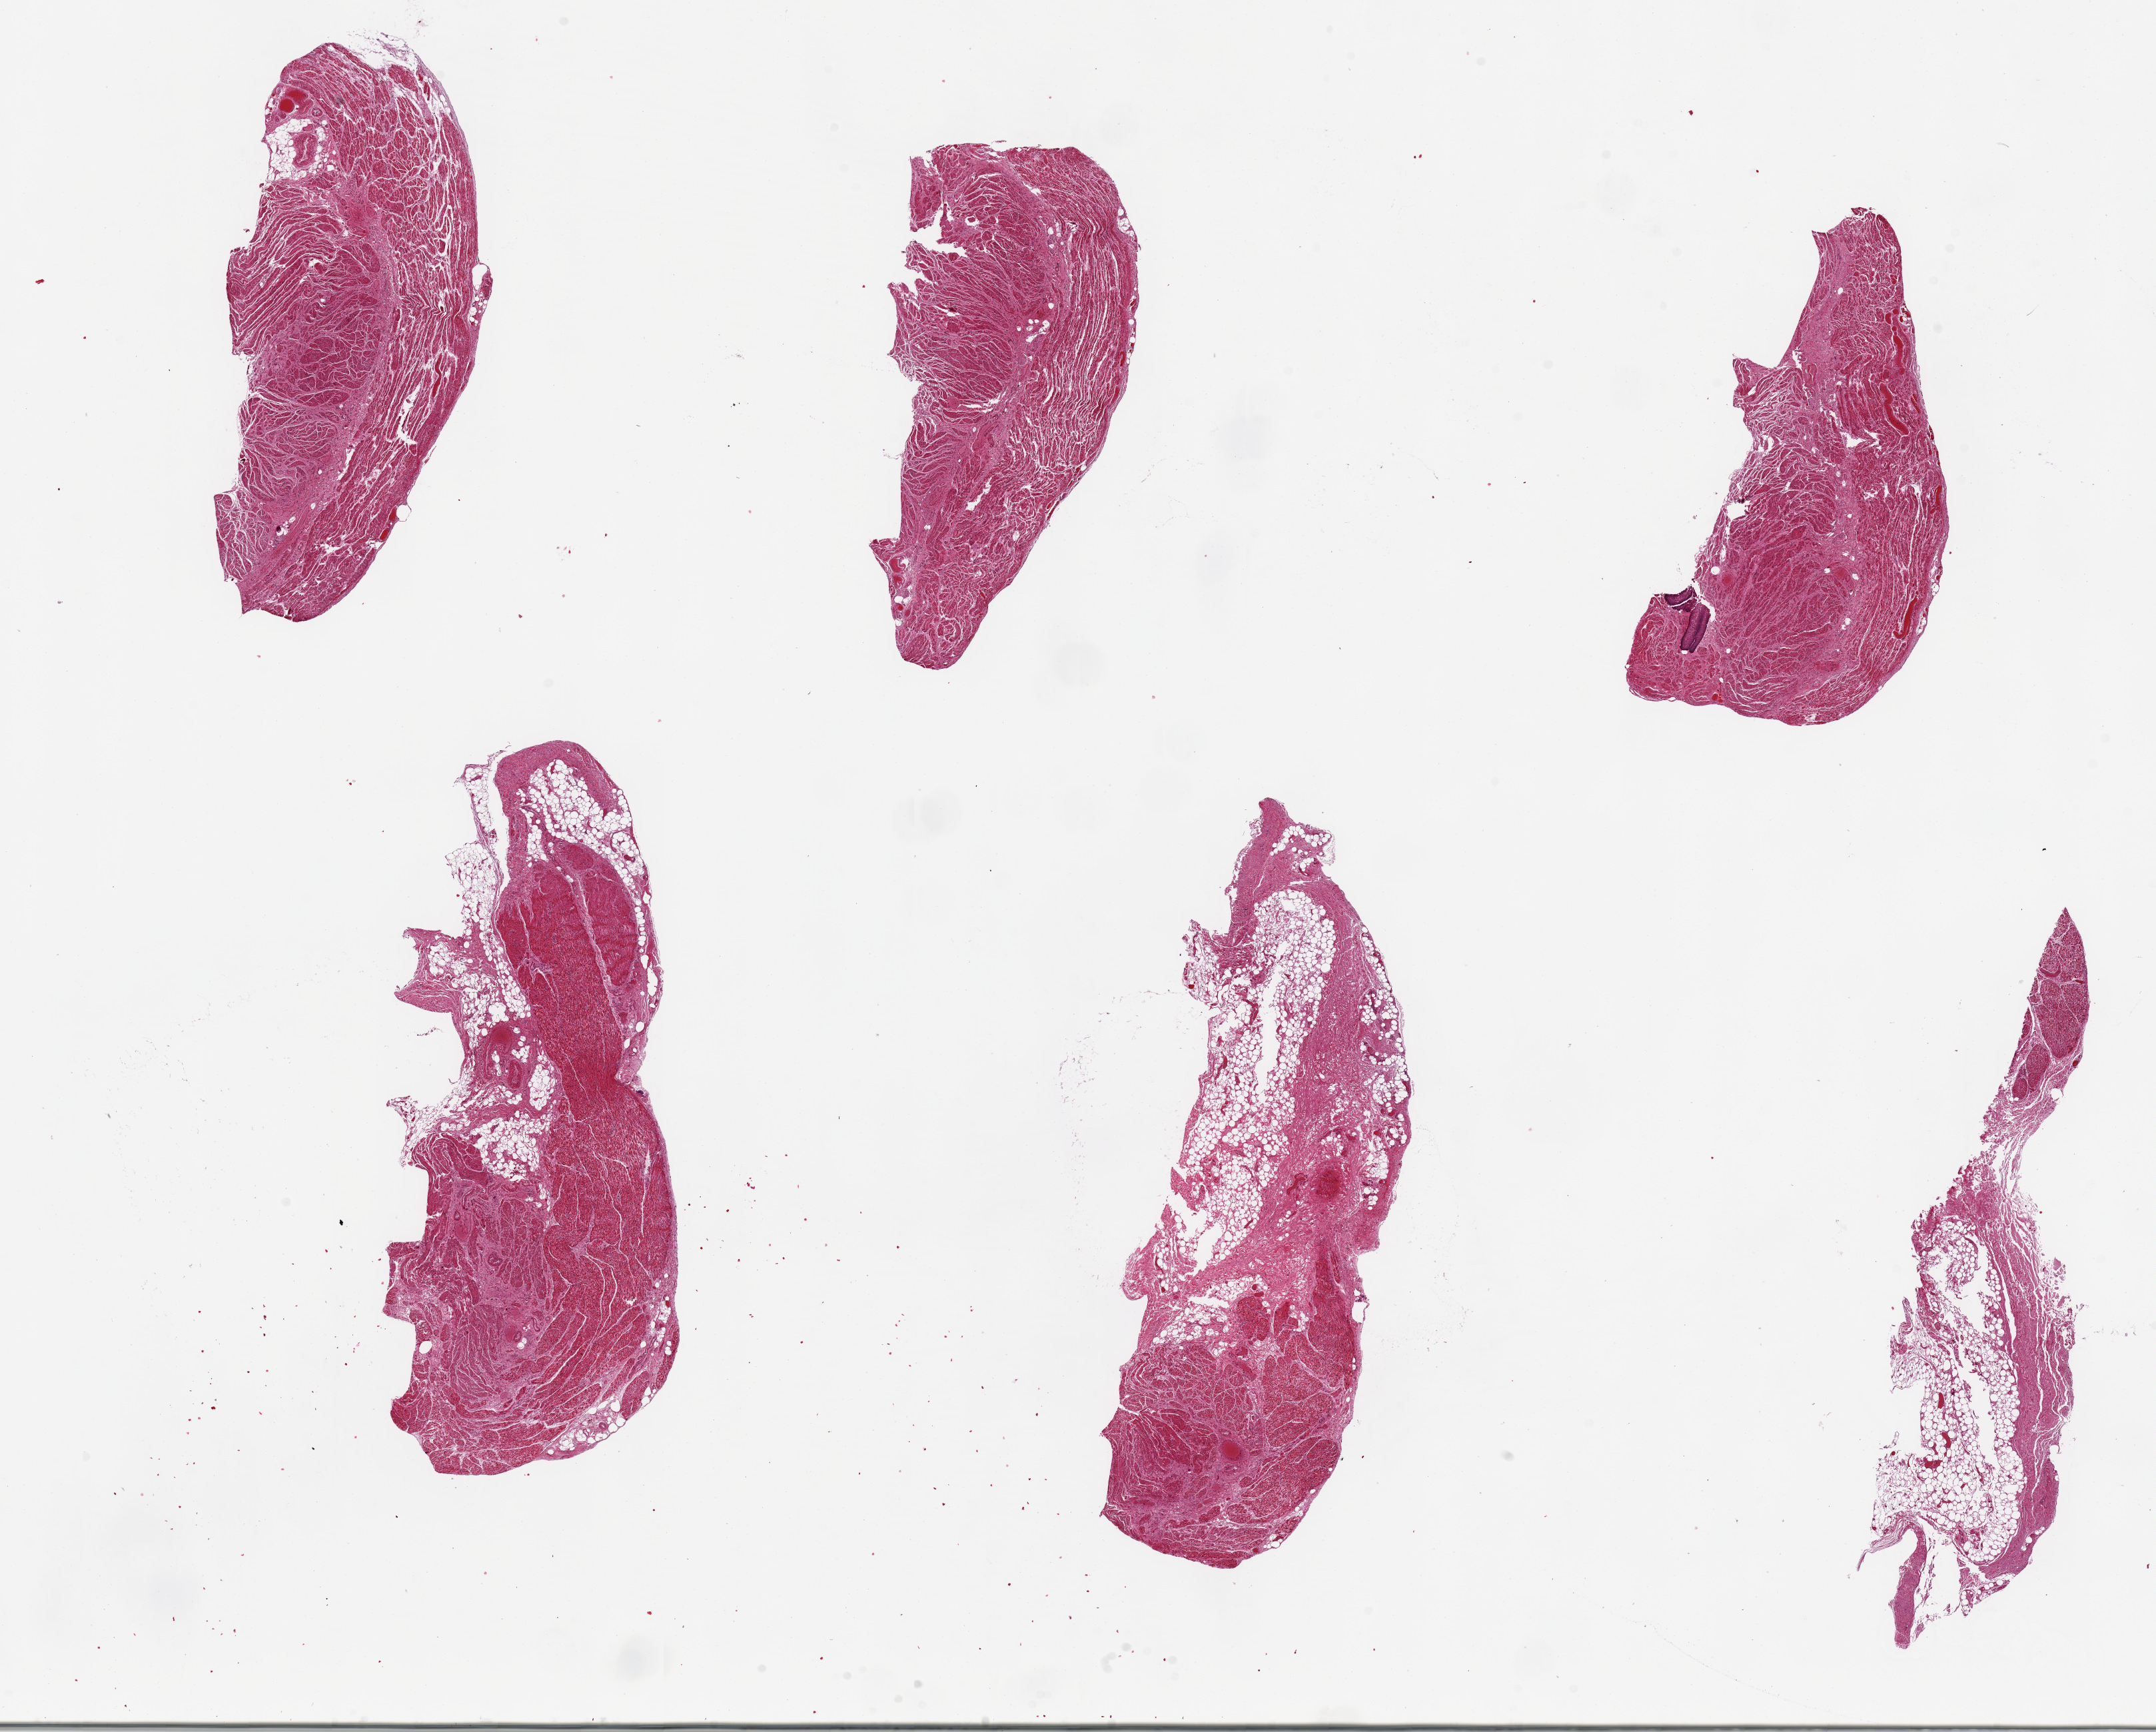
Digitized hematoxylin and eosin (H&E)-stained section — low-resolution overview of the scanned area, about 25.6 x 20.6 mm (from a 20x scan). PAXgene-fixed, paraffin-embedded tissue. Sampled site (target tissue): gastroesophageal junction. Donor tissue sample. Donor: male.
Review note (as recorded): 6 pieces, up to 9x3mm; all muscle, small squamous mucosal 'floater'.